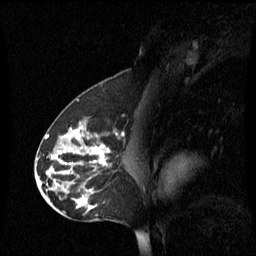
Breast MRI (dynamic contrast-enhanced), one sagittal slice. Slice 35 of 60 in the series (ordered by position). Dynamic contrast-enhanced series, image 2 of 3 at this slice position (ordered by acquisition). 1.5 T. TE 4.2 ms, TR 8.4 ms. 2.2 mm slice thickness. 256 × 256 image matrix, field of view 240 × 240 mm. Female patient, age 45 years. Case-level facts recorded for this patient, not image findings: setting: breast cancer imaged before/during neoadjuvant chemotherapy; receptor status: HR-positive, HER2-negative.
Outlined on this slice (semi-automatically segmented with operator editing):
- analysis volume of interest (the breast-tissue region the enhancement analysis was run in; not a lesion): bounding box [x1, y1, x2, y2] px = [38, 120, 131, 221]
- tumour enhancement mask (voxels above the 70 % enhancement threshold inside the analysis volume of interest): [54, 128, 109, 165]